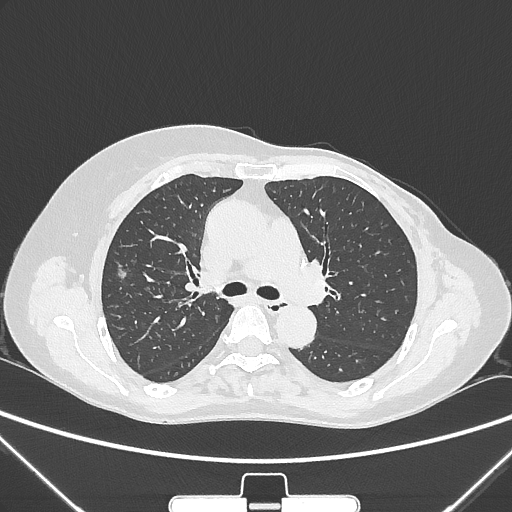
Chest CT, one axial slice; position 163 of 265 along the scan axis; 120 kVp; lung window (W 1500 / L -600 HU); 1 mm slice thickness; 512 × 512 image matrix. Female patient, age 64 years. From the clinical record (not read from this slice): clinical TNM (as recorded): T1c N0 M0; histopathological grade: G1-2.
Outlined on this slice (bounding box drawn by a radiologist):
- lung tumour (recorded histology: adenocarcinoma): box from (x=111, y=265) to (x=131, y=288) px